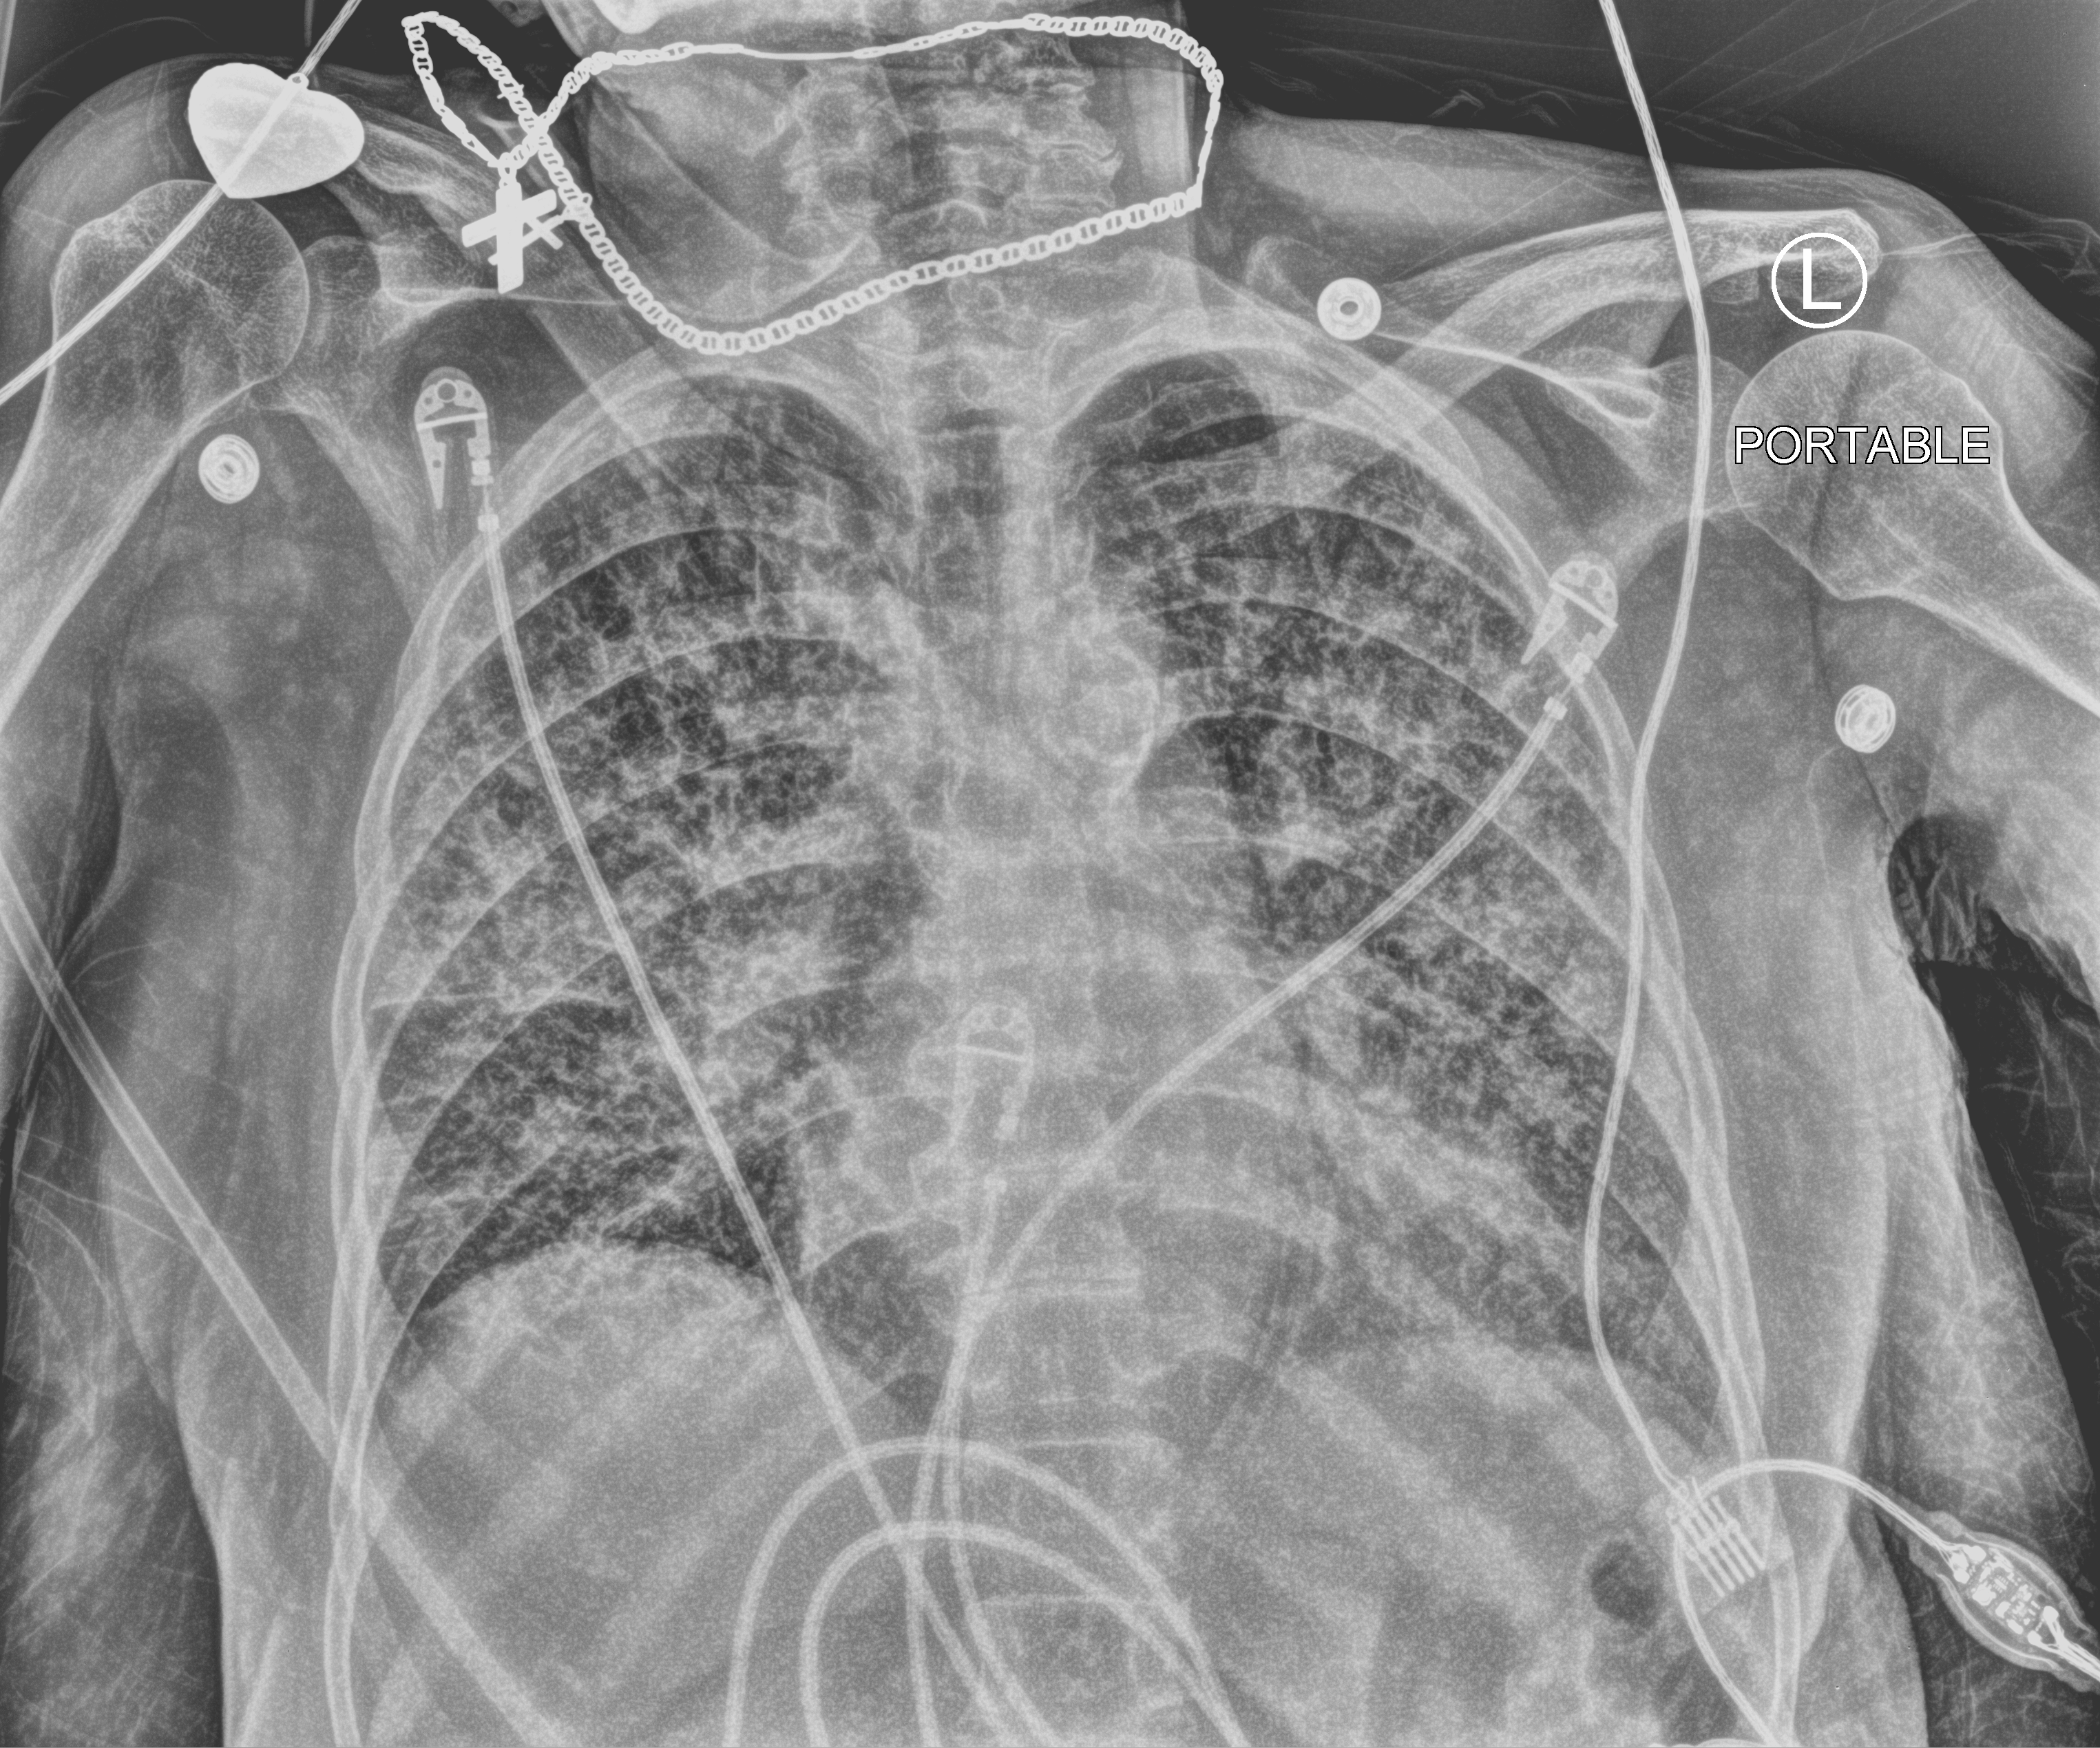
Portable chest radiograph, anteroposterior (AP) projection. Patient hospitalised with COVID-19; female, aged 75–90 years.
Admission-level facts for this patient (not findings on this image; timing relative to this image not recorded): hypertension (admission record): yes; smoking status (admission record): never.